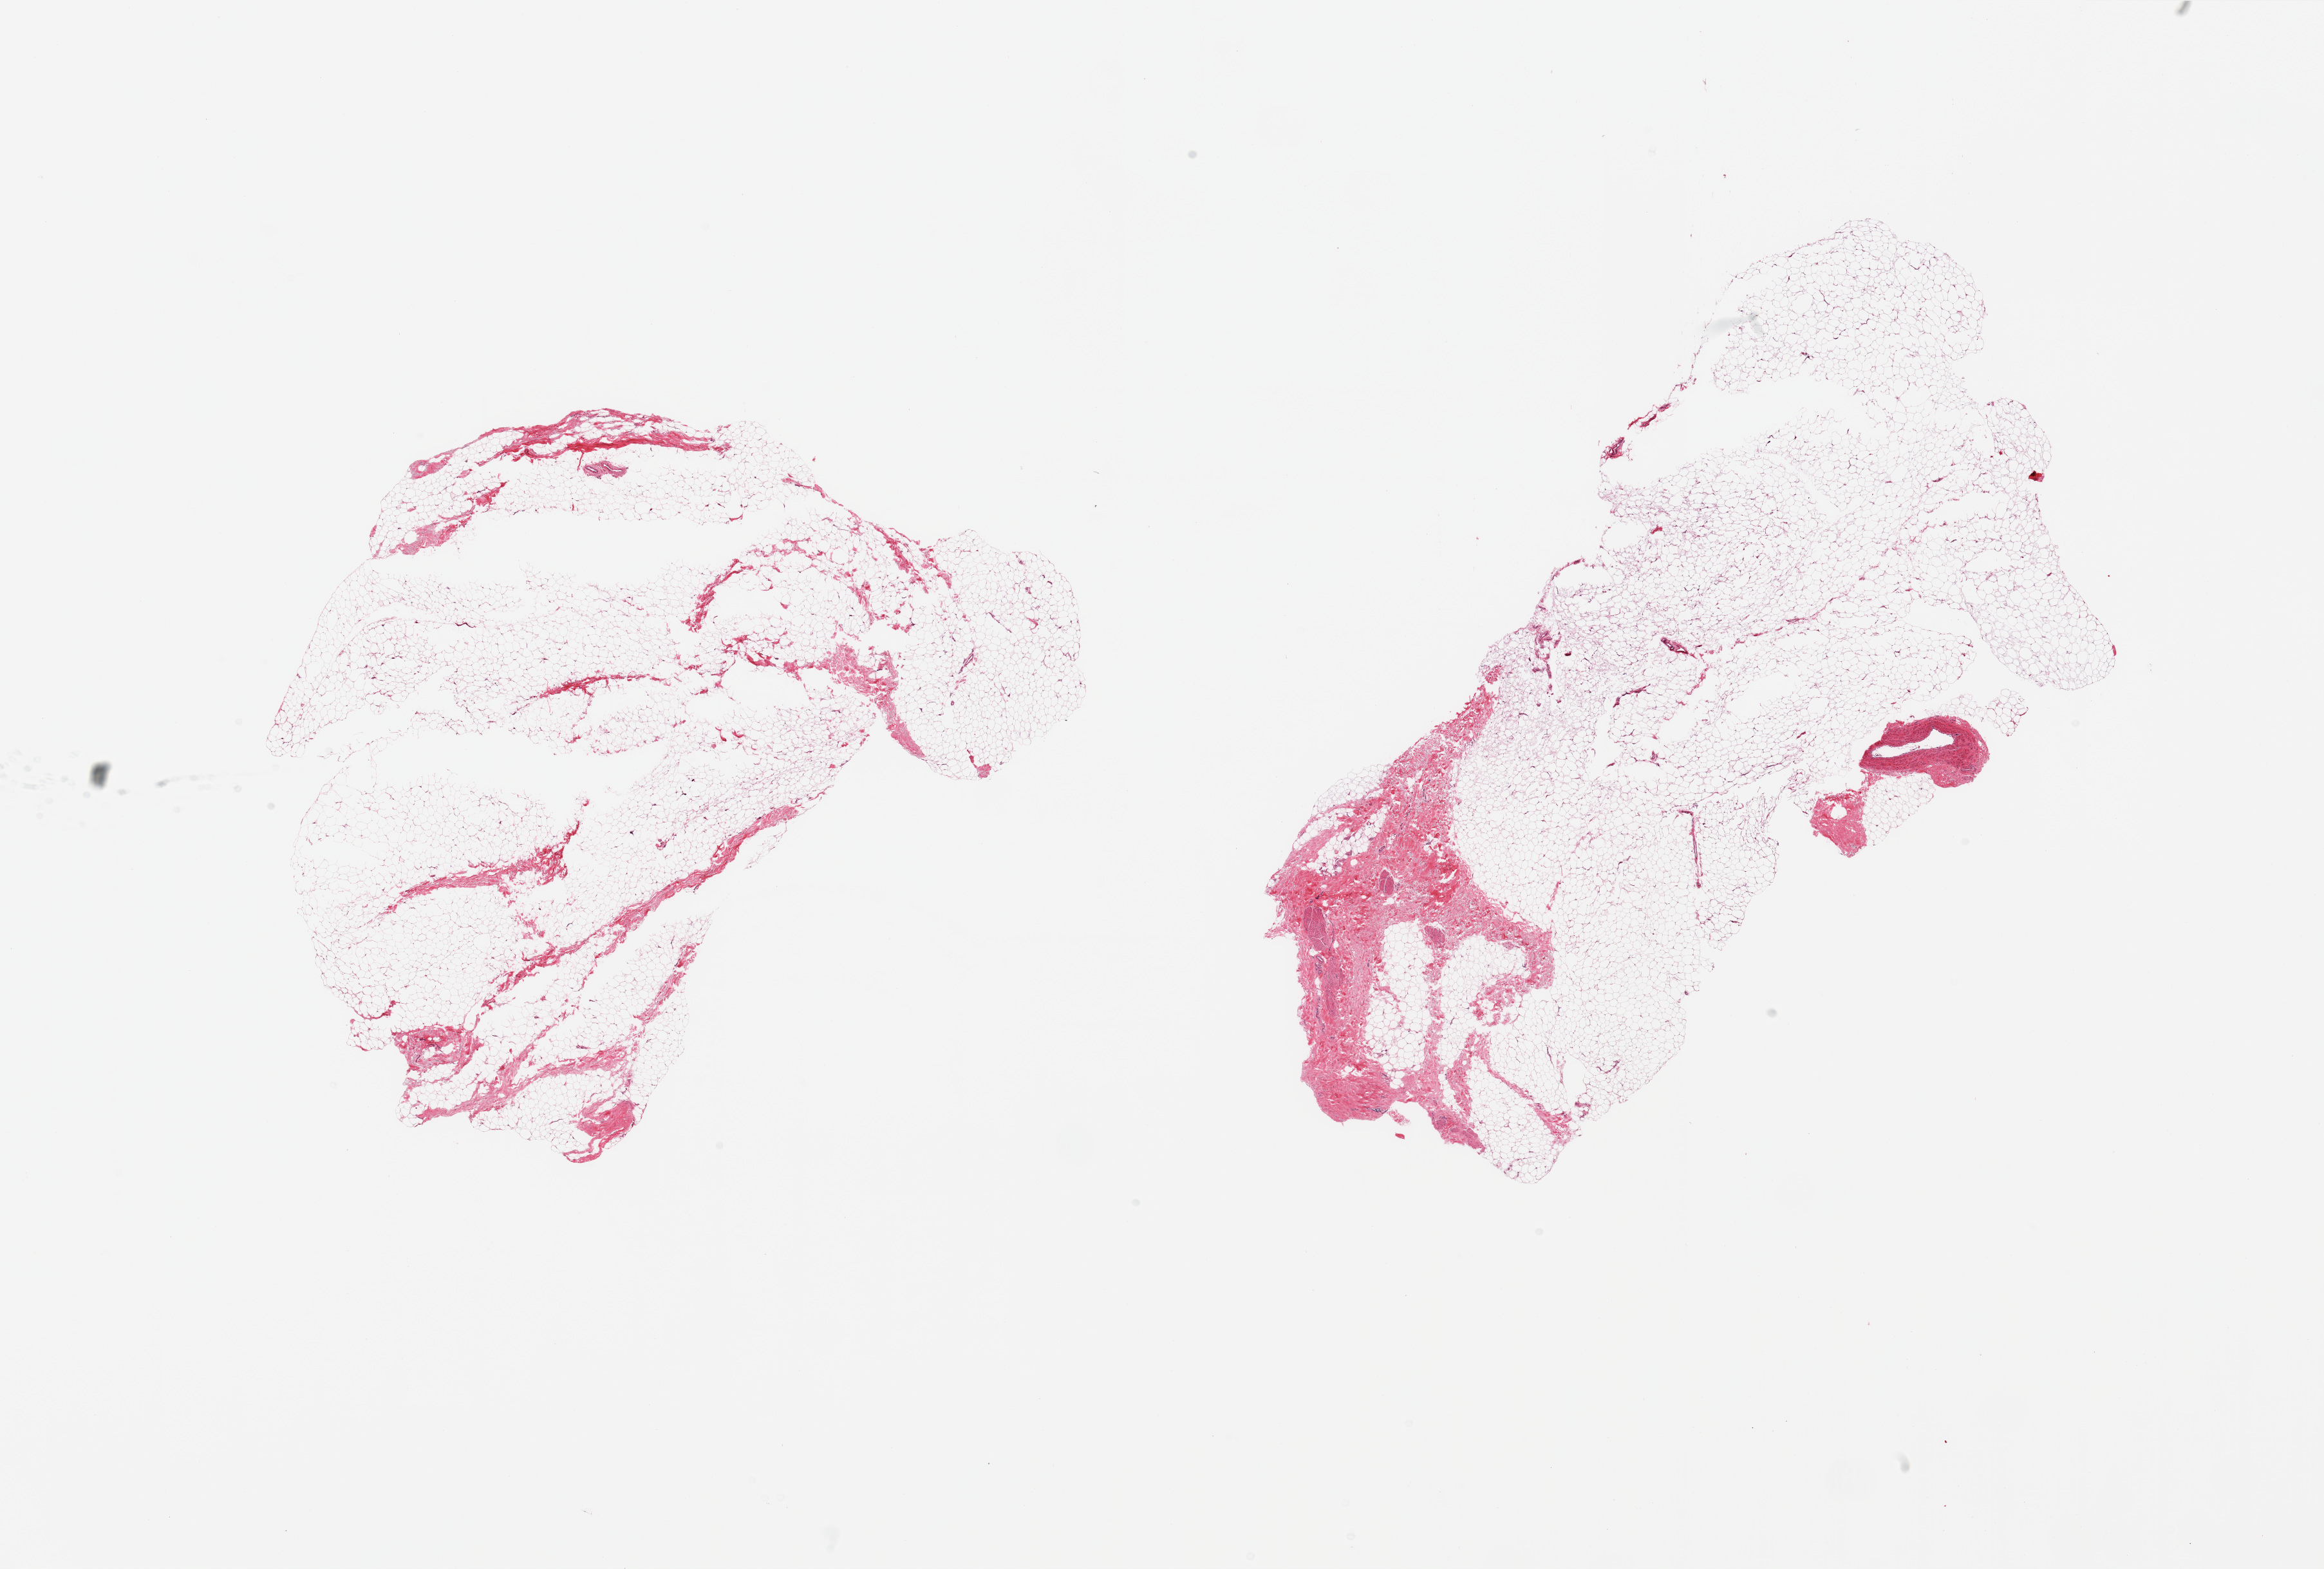
Digitized hematoxylin and eosin (H&E)-stained section, a low-resolution overview of the entire scanned area, about 28.5 x 19.3 mm, PAXgene-fixed paraffin-embedded (PFPE) section, section of breast (target tissue), tissue donor sample. Donor: male.
Pathologist's review note for this sample: 2 pieces, all fibroadipose elements, no ductal structures noted.